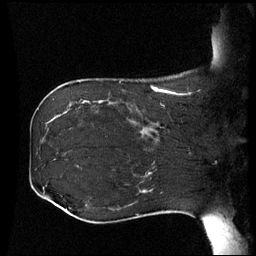
Breast MRI (dynamic contrast-enhanced), one sagittal slice; position 18 of 60 along the scan axis; dynamic contrast-enhanced series, image 2 of 3 at this slice position (ordered by acquisition); 1.5 T; TE 4.2 ms, TR 8.9 ms; 2.5 mm slice thickness; 256 × 256 image matrix, field of view 230 × 230 mm. Patient: female, 42 years. From the clinical record (not read from this slice): setting: breast cancer imaged before/during neoadjuvant chemotherapy; receptor status: HER2-positive.
Structures marked on this image (semi-automatic segmentation, software-assisted and operator-edited):
- analysis volume of interest (the breast-tissue region the enhancement analysis was run in; not a lesion): bounding box [x1, y1, x2, y2] px = [106, 102, 173, 150]
- tumour enhancement mask (voxels above the 70 % enhancement threshold inside the analysis volume of interest): [140, 131, 157, 137]